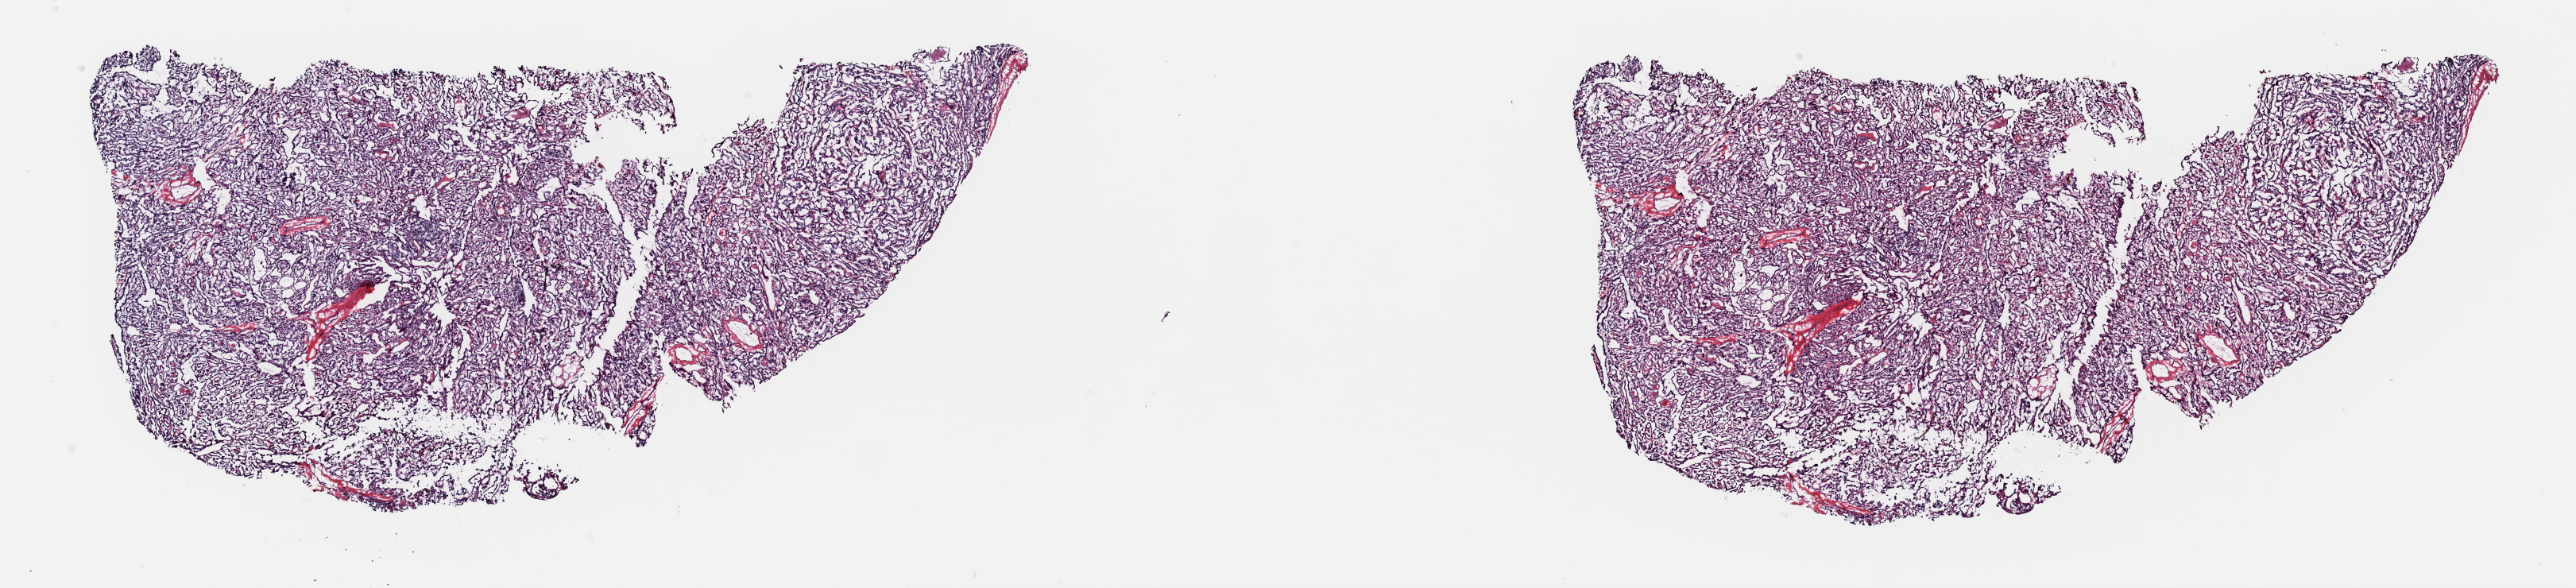
Whole-slide histology image, H&E — low-resolution overview of the scanned area, about 25.6 x 5.8 mm; frozen section from the top of the tissue portion; sample: primary tumour, thyroid. Patient: female, age at initial diagnosis 78 years. Composition of this section per pathologist review: tumour cells 100%, tumour nuclei 93%.
Pathologic diagnosis: Papillary adenocarcinoma, NOS (thyroid gland).